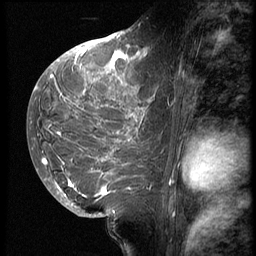
Breast MRI (dynamic contrast-enhanced), one sagittal slice. Position 28 of 62 along the scan axis. 3 images stored at this slice position (order not interpretable as contrast timing). 1.5 T. TE 4.2 ms, TR 9 ms. 2.5 mm slice thickness. 256 × 256 image matrix, field of view 180 × 180 mm. Female patient, age 28 years. Case-level facts recorded for this patient, not image findings: setting: breast cancer imaged before/during neoadjuvant chemotherapy.
Outlined on this slice (semi-automatically segmented with operator editing):
- analysis volume of interest (the breast-tissue region the enhancement analysis was run in; not a lesion): bounding box (x1, y1, x2, y2) in pixels: (42, 45, 164, 207)
- tumour enhancement mask (voxels above the 140 % enhancement threshold inside the analysis volume of interest): (42, 46, 148, 198)